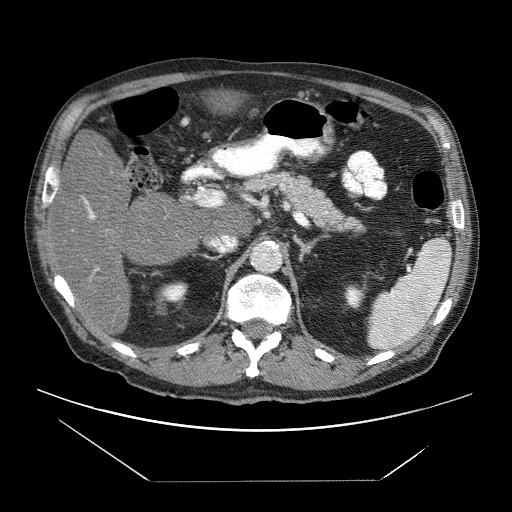
Contrast-enhanced abdominal CT (liver protocol), one axial slice. Position 31 of 83 along the scan axis. Soft-tissue window (W 400 / L 40 HU). 512 × 512 image matrix, field of view 420 × 420 mm. From the clinical record (not read from this slice): diagnosis: hepatocellular carcinoma (patient treated with transarterial chemoembolisation; whether this scan precedes or follows treatment is not stated here); TNM stage (as recorded): Stage-IVB; Child-Pugh class: B; tumour nodularity: uninodular.
Outlined on this slice (semi-automatically segmented with operator editing):
- liver parenchyma outside the tumour (the mass and vessels are separate outlines, so this box may not span the whole liver): box from (x=56, y=89) to (x=255, y=298) px
- liver vessels: (x=83, y=197)–(x=98, y=271)